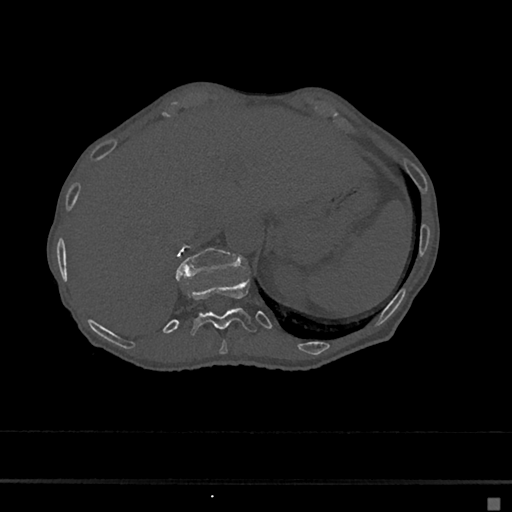
CT including the spine, one axial slice; slice 169 of 797 in the series (ordered by position); reconstruction kernel Br40s/3; bone window (W 1800 / L 400 HU); 0.5 mm slice thickness; 512 × 512 image matrix, field of view 360 × 360 mm. Female patient, age 68 years. From the clinical record (not read from this slice): primary cancer: renal.
Outlined on this slice (semi-automatic segmentation, software-assisted and operator-edited):
- T10 vertebra: bounding box <219,340,228,355> (left, top, right, bottom; pixels)
- T11 vertebra: <183,278,257,337>
- T12 vertebra: <175,247,240,279>